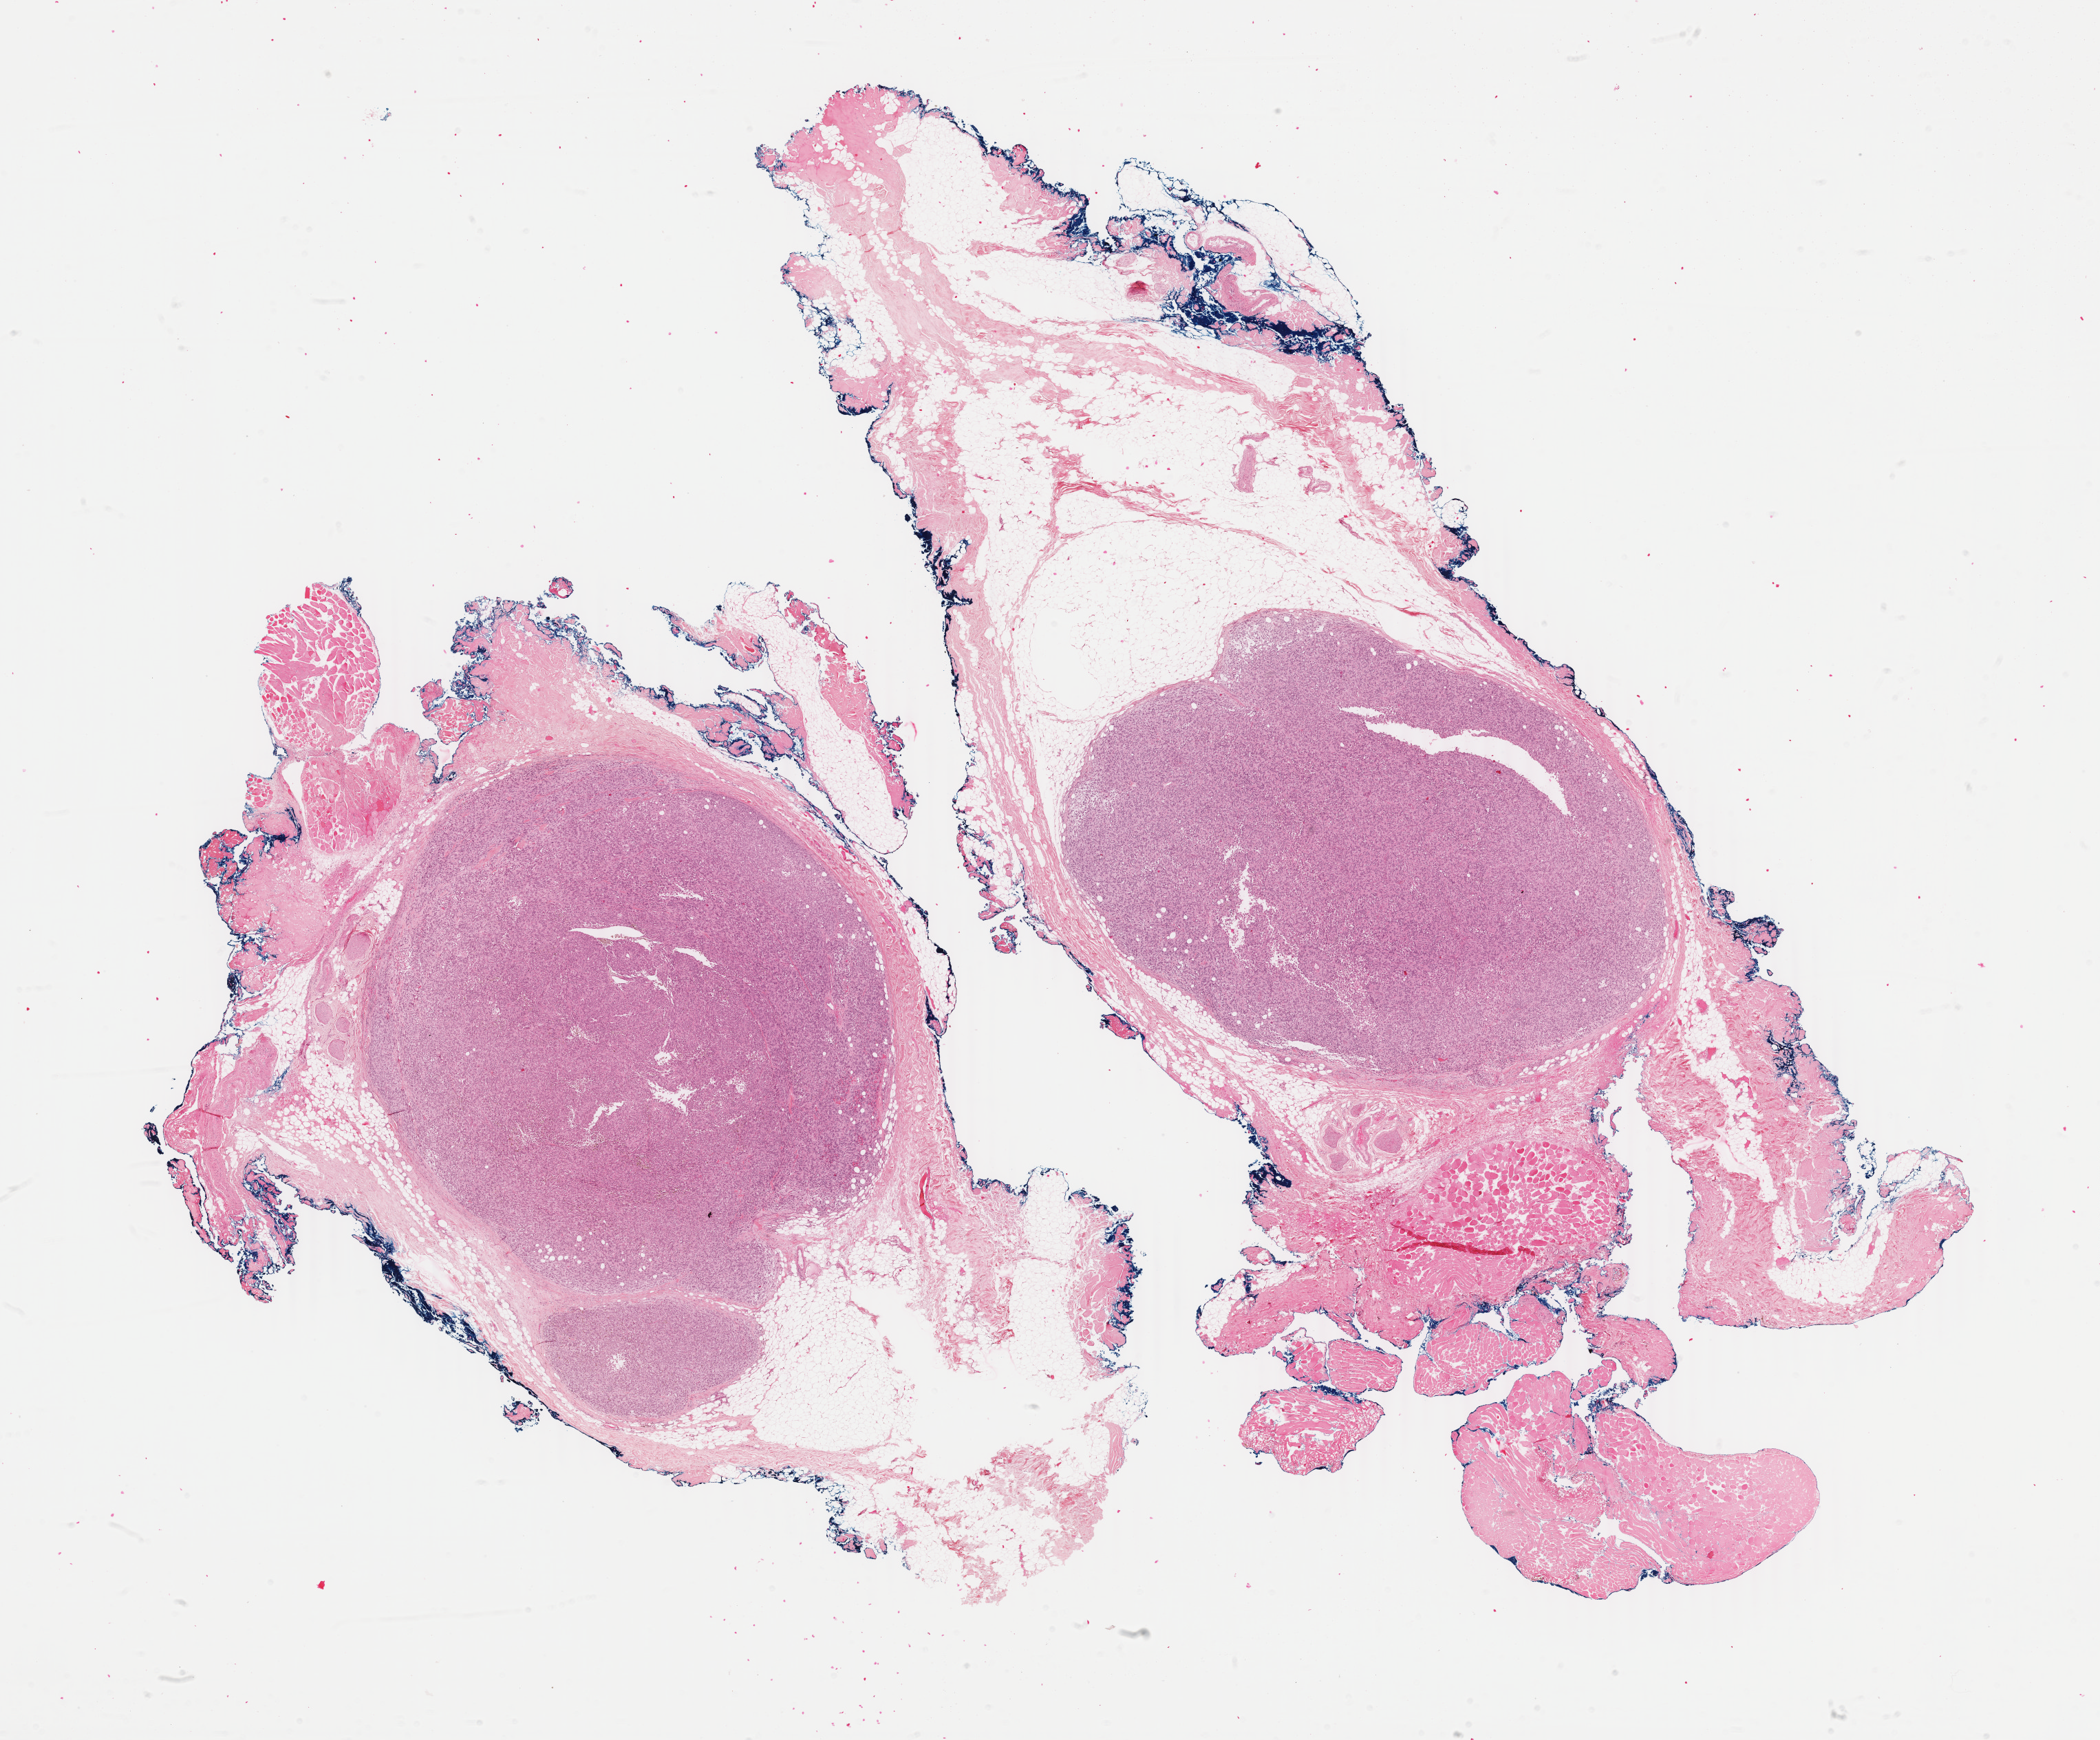
Whole-slide histology image, H&E-stained, shown as a low-resolution overview of the whole scanned area (about 24.3 x 20.1 mm), formalin-fixed paraffin-embedded (FFPE) diagnostic section, skin, primary tumour sample. Male patient; age at initial diagnosis 87 years.
Pathologic diagnosis: Malignant melanoma, NOS.